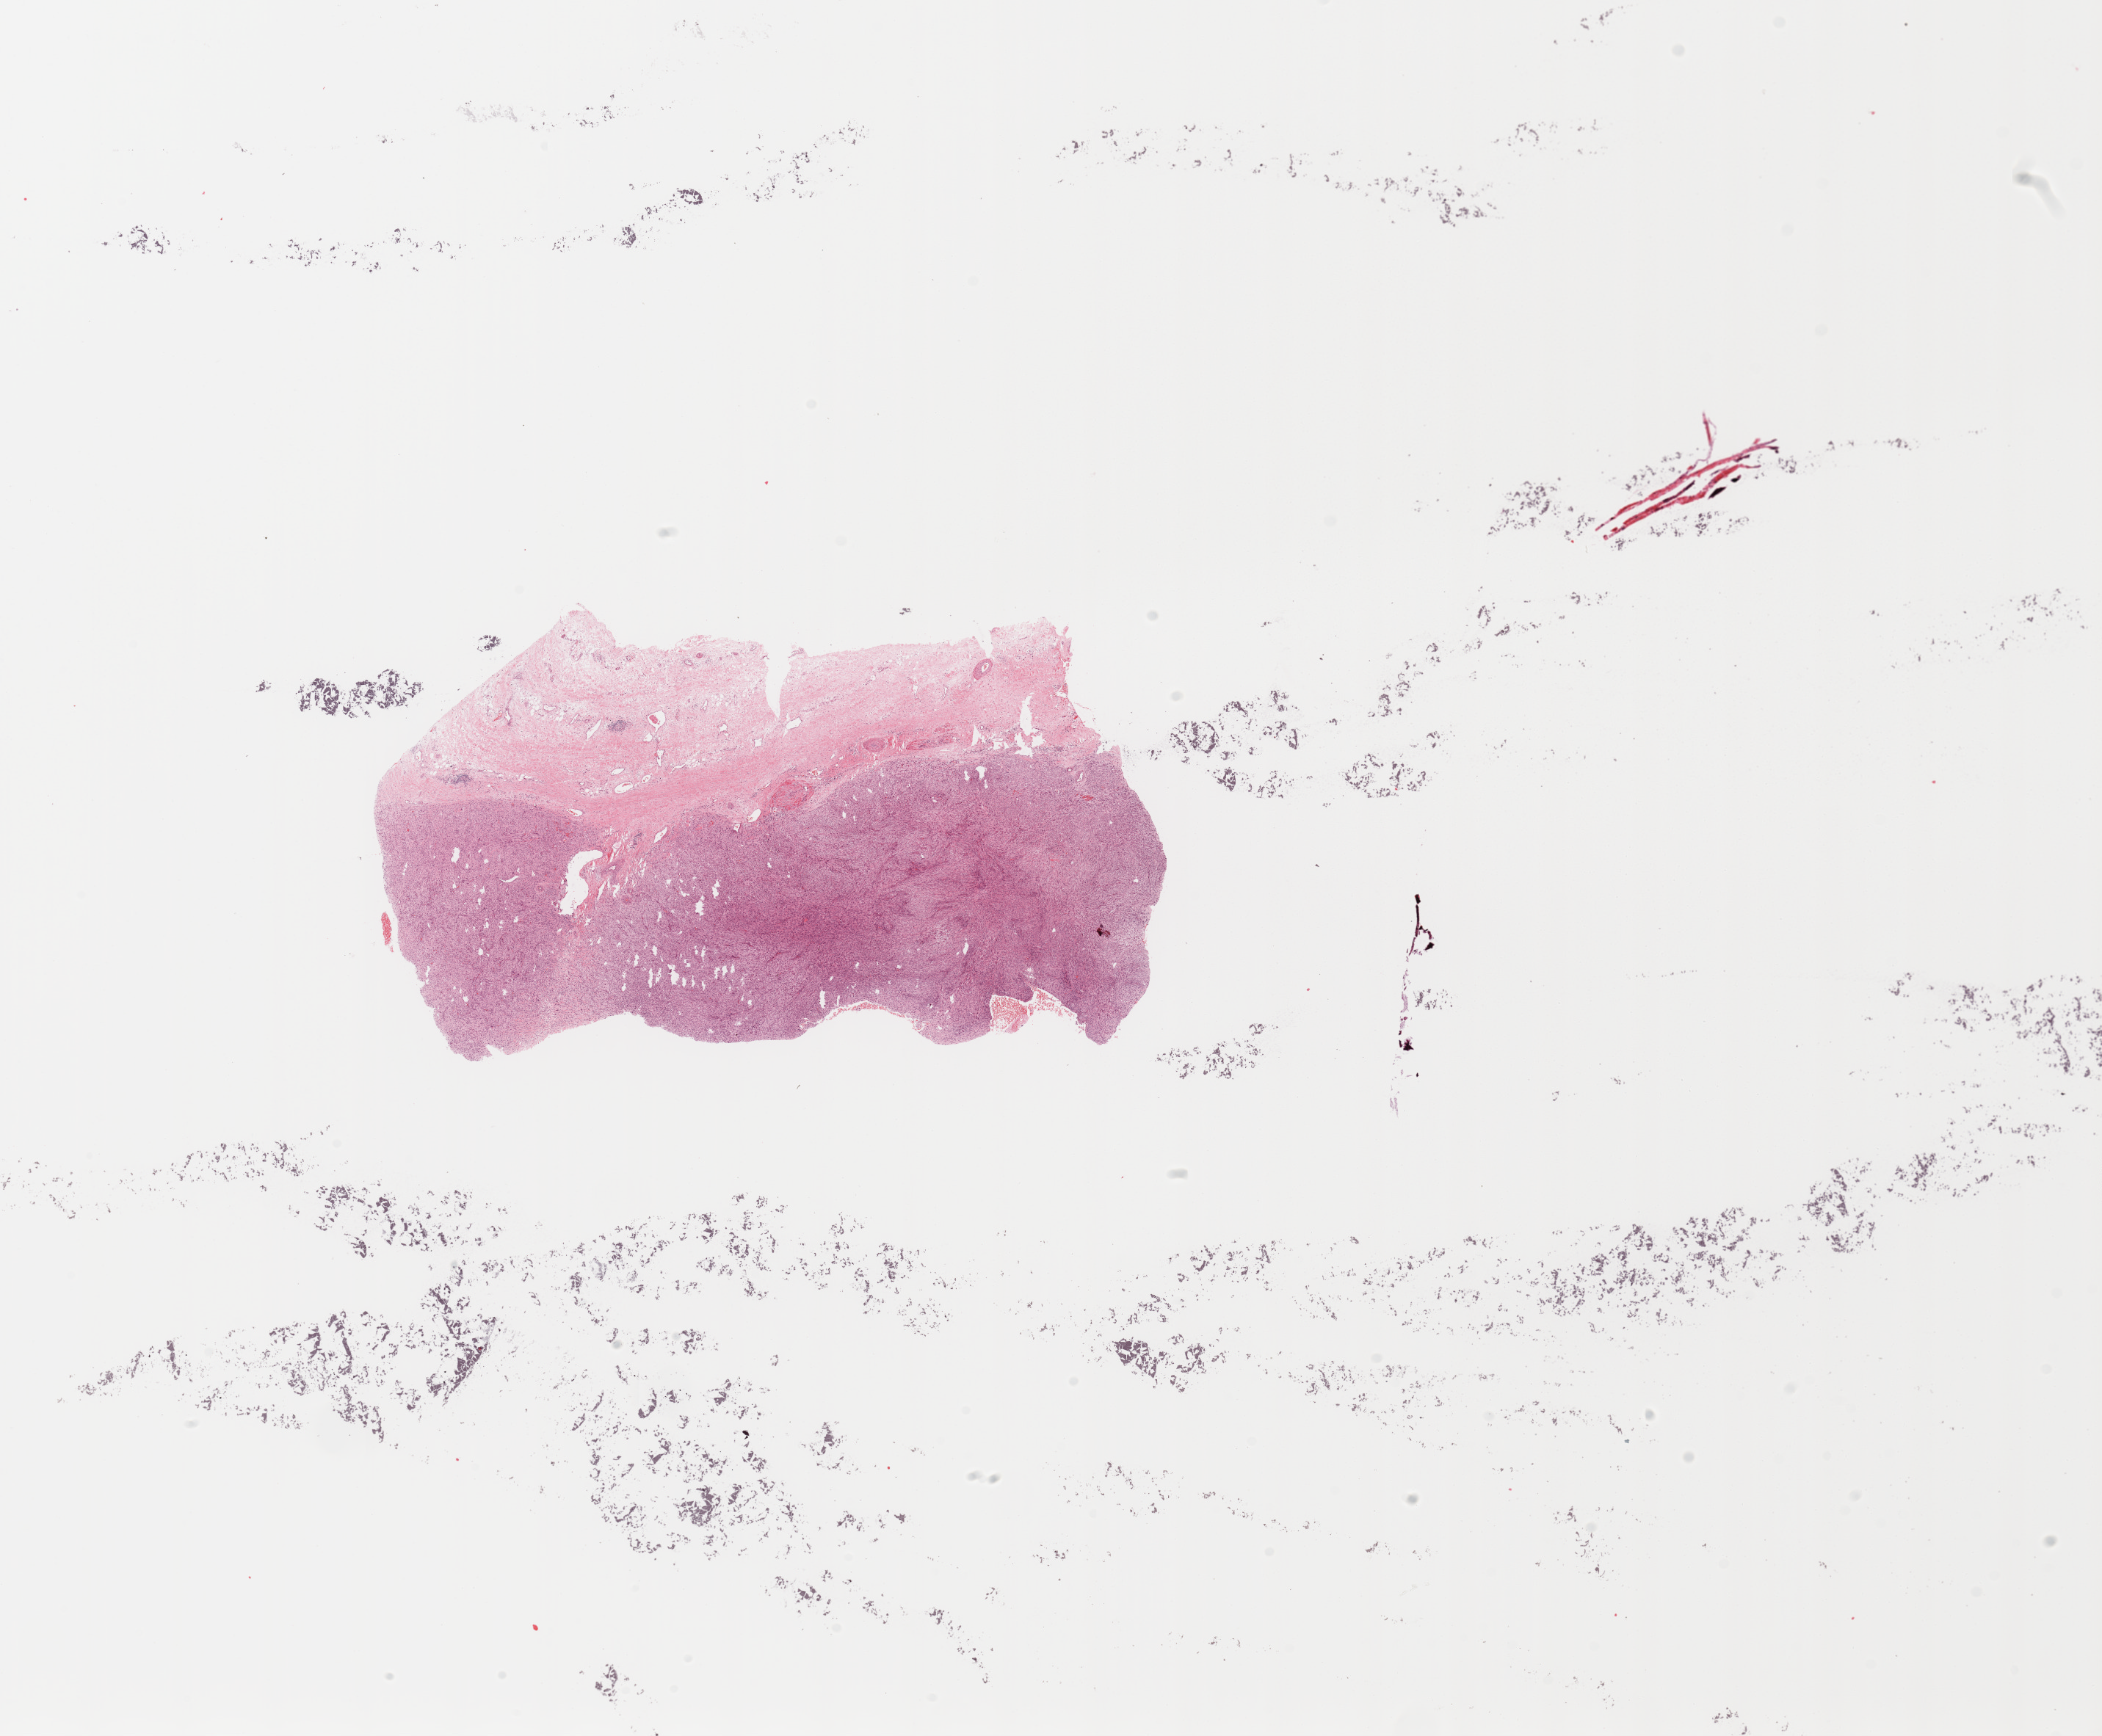
Digitized Hematoxylin and eosin (H&E) stained tissue section (whole slide) — a low-resolution overview of the entire scanned area, about 22.6 x 18.7 mm; tumour tissue sample. Patient: male, age 67 years.
• primary tumour site (as recorded): lower extremity
• patient diagnosis (cohort enrolment): sarcoma (site not recorded at cohort level)